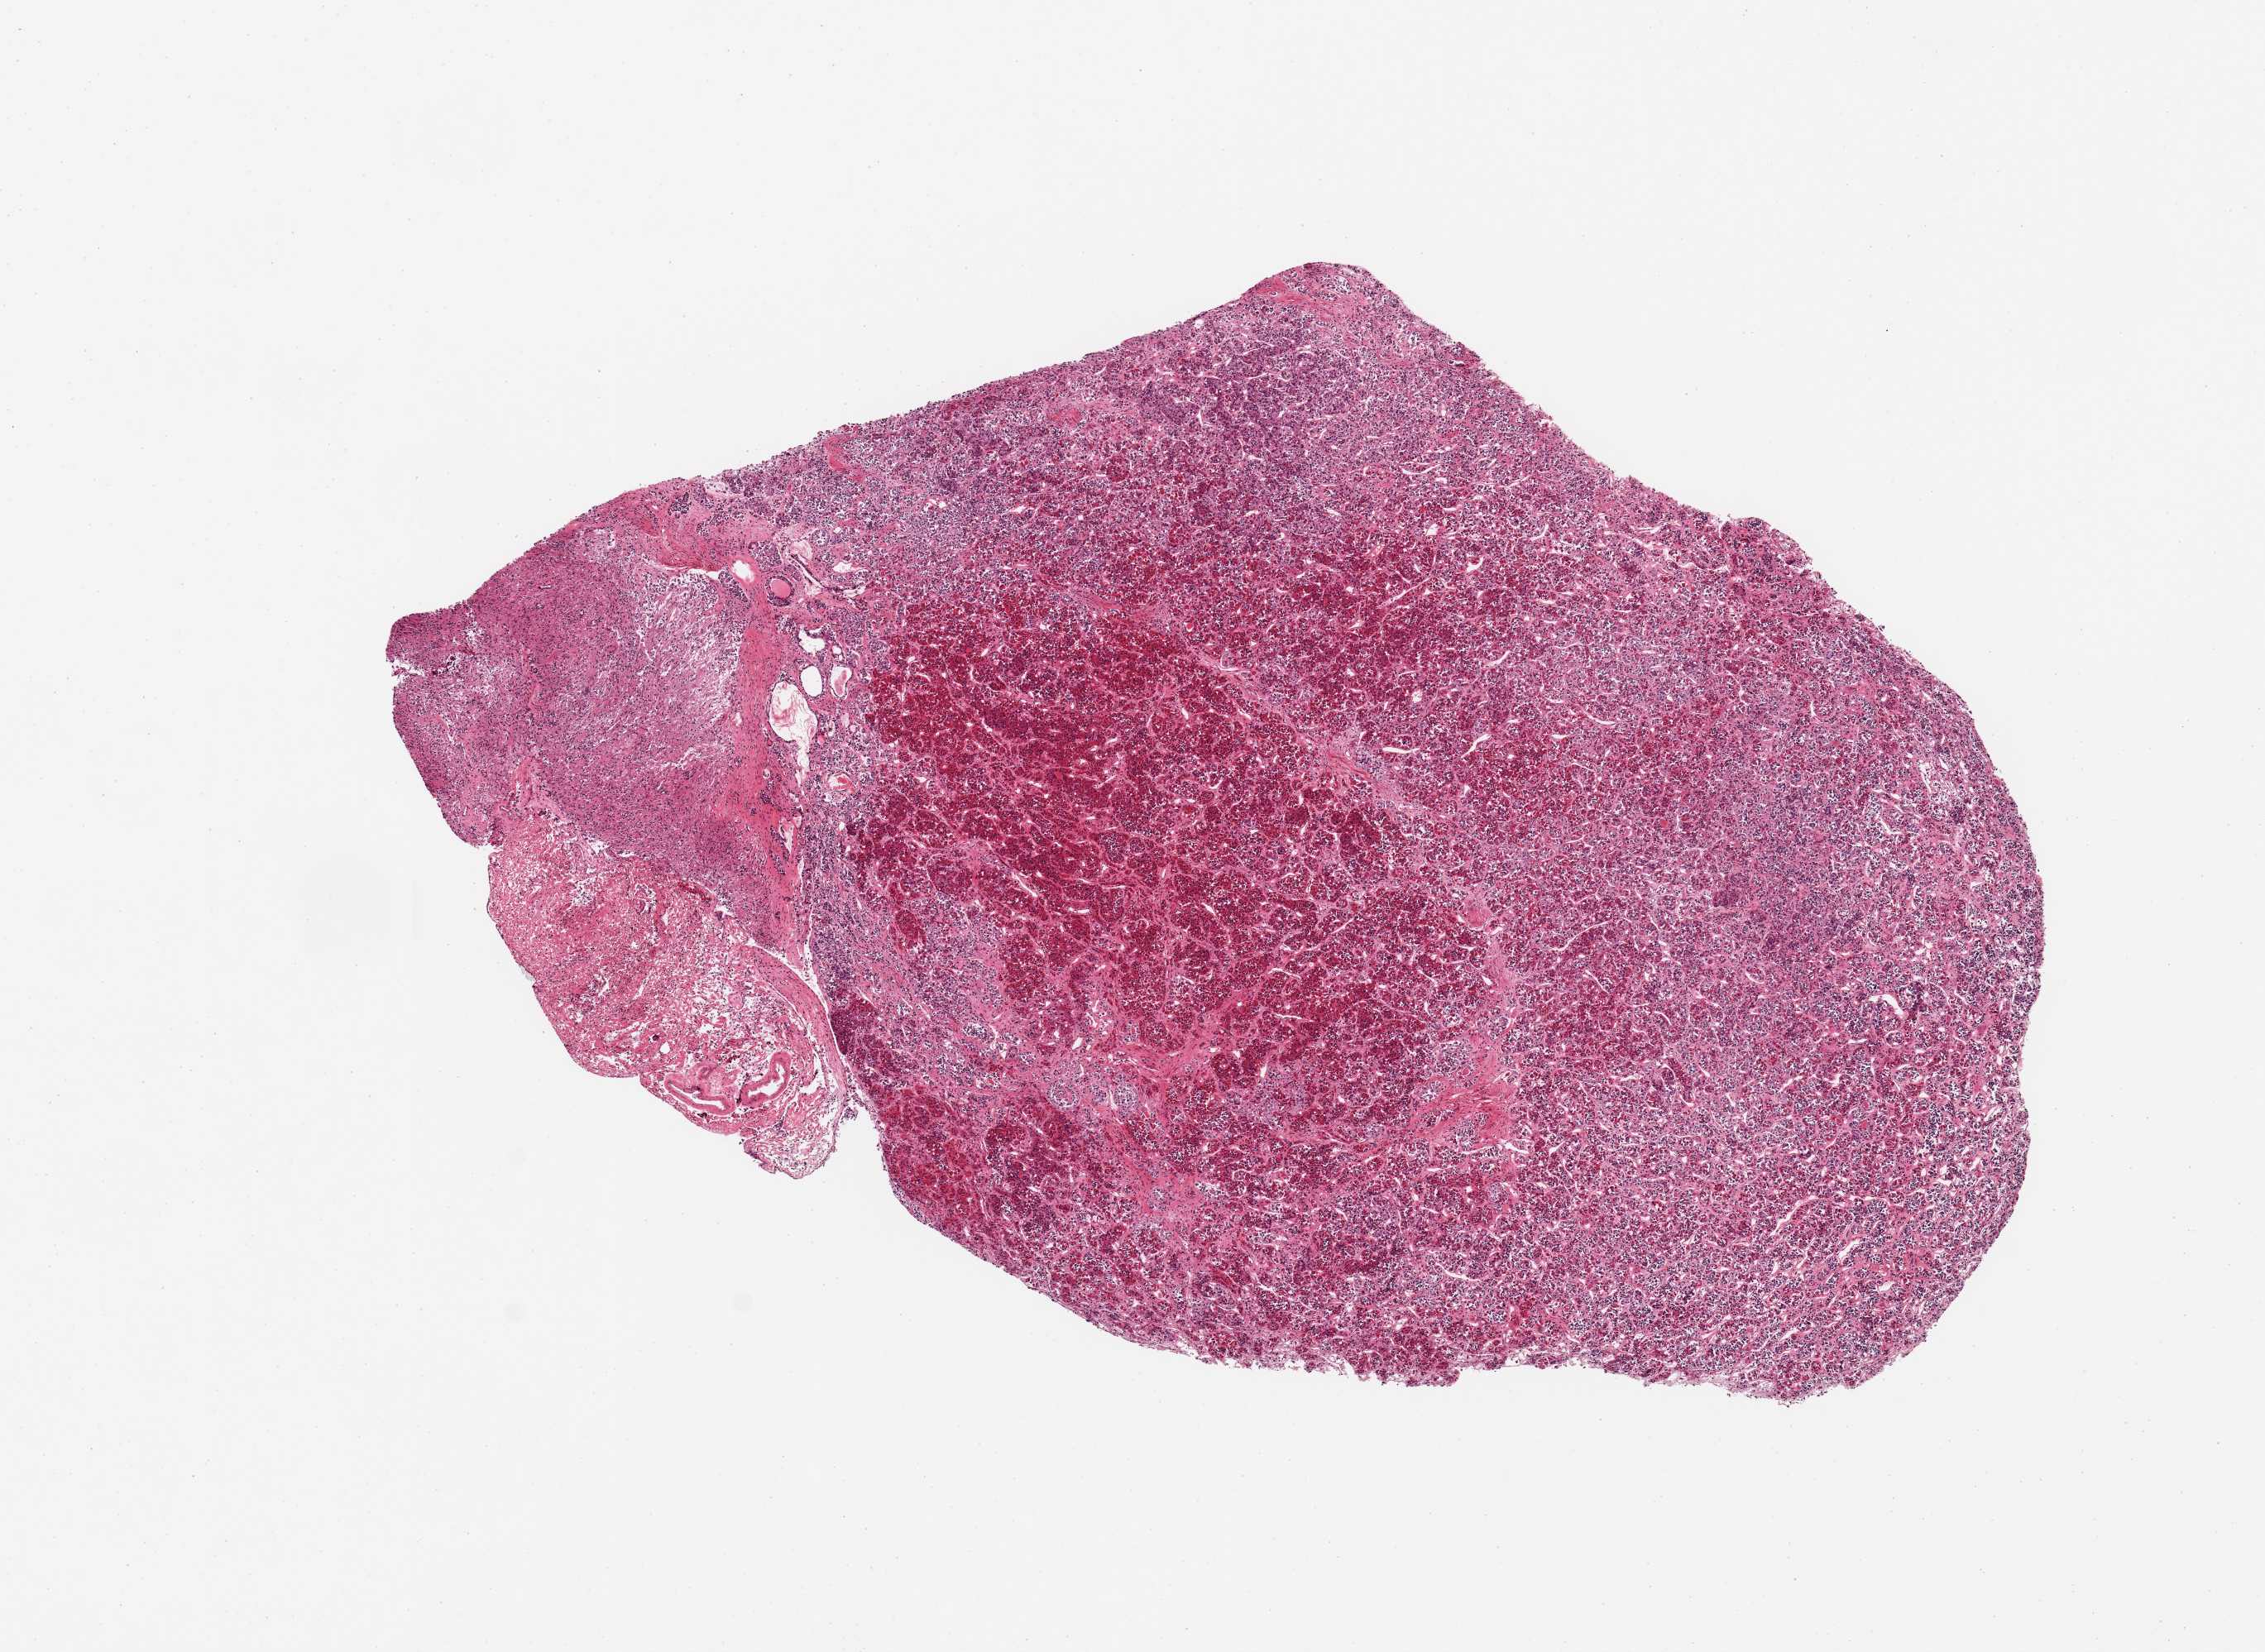
Whole-slide image, haematoxylin and eosin stain, brightfield, whole scanned area (about 10.8 x 7.9 mm) shown as a low-resolution overview, PAXgene-fixed, paraffin-embedded tissue, sampled site (target tissue): pituitary, tissue donor sample. Donor: male.
- reviewer comment on this tissue sample: 1 piece, ~20% neurohypophysis